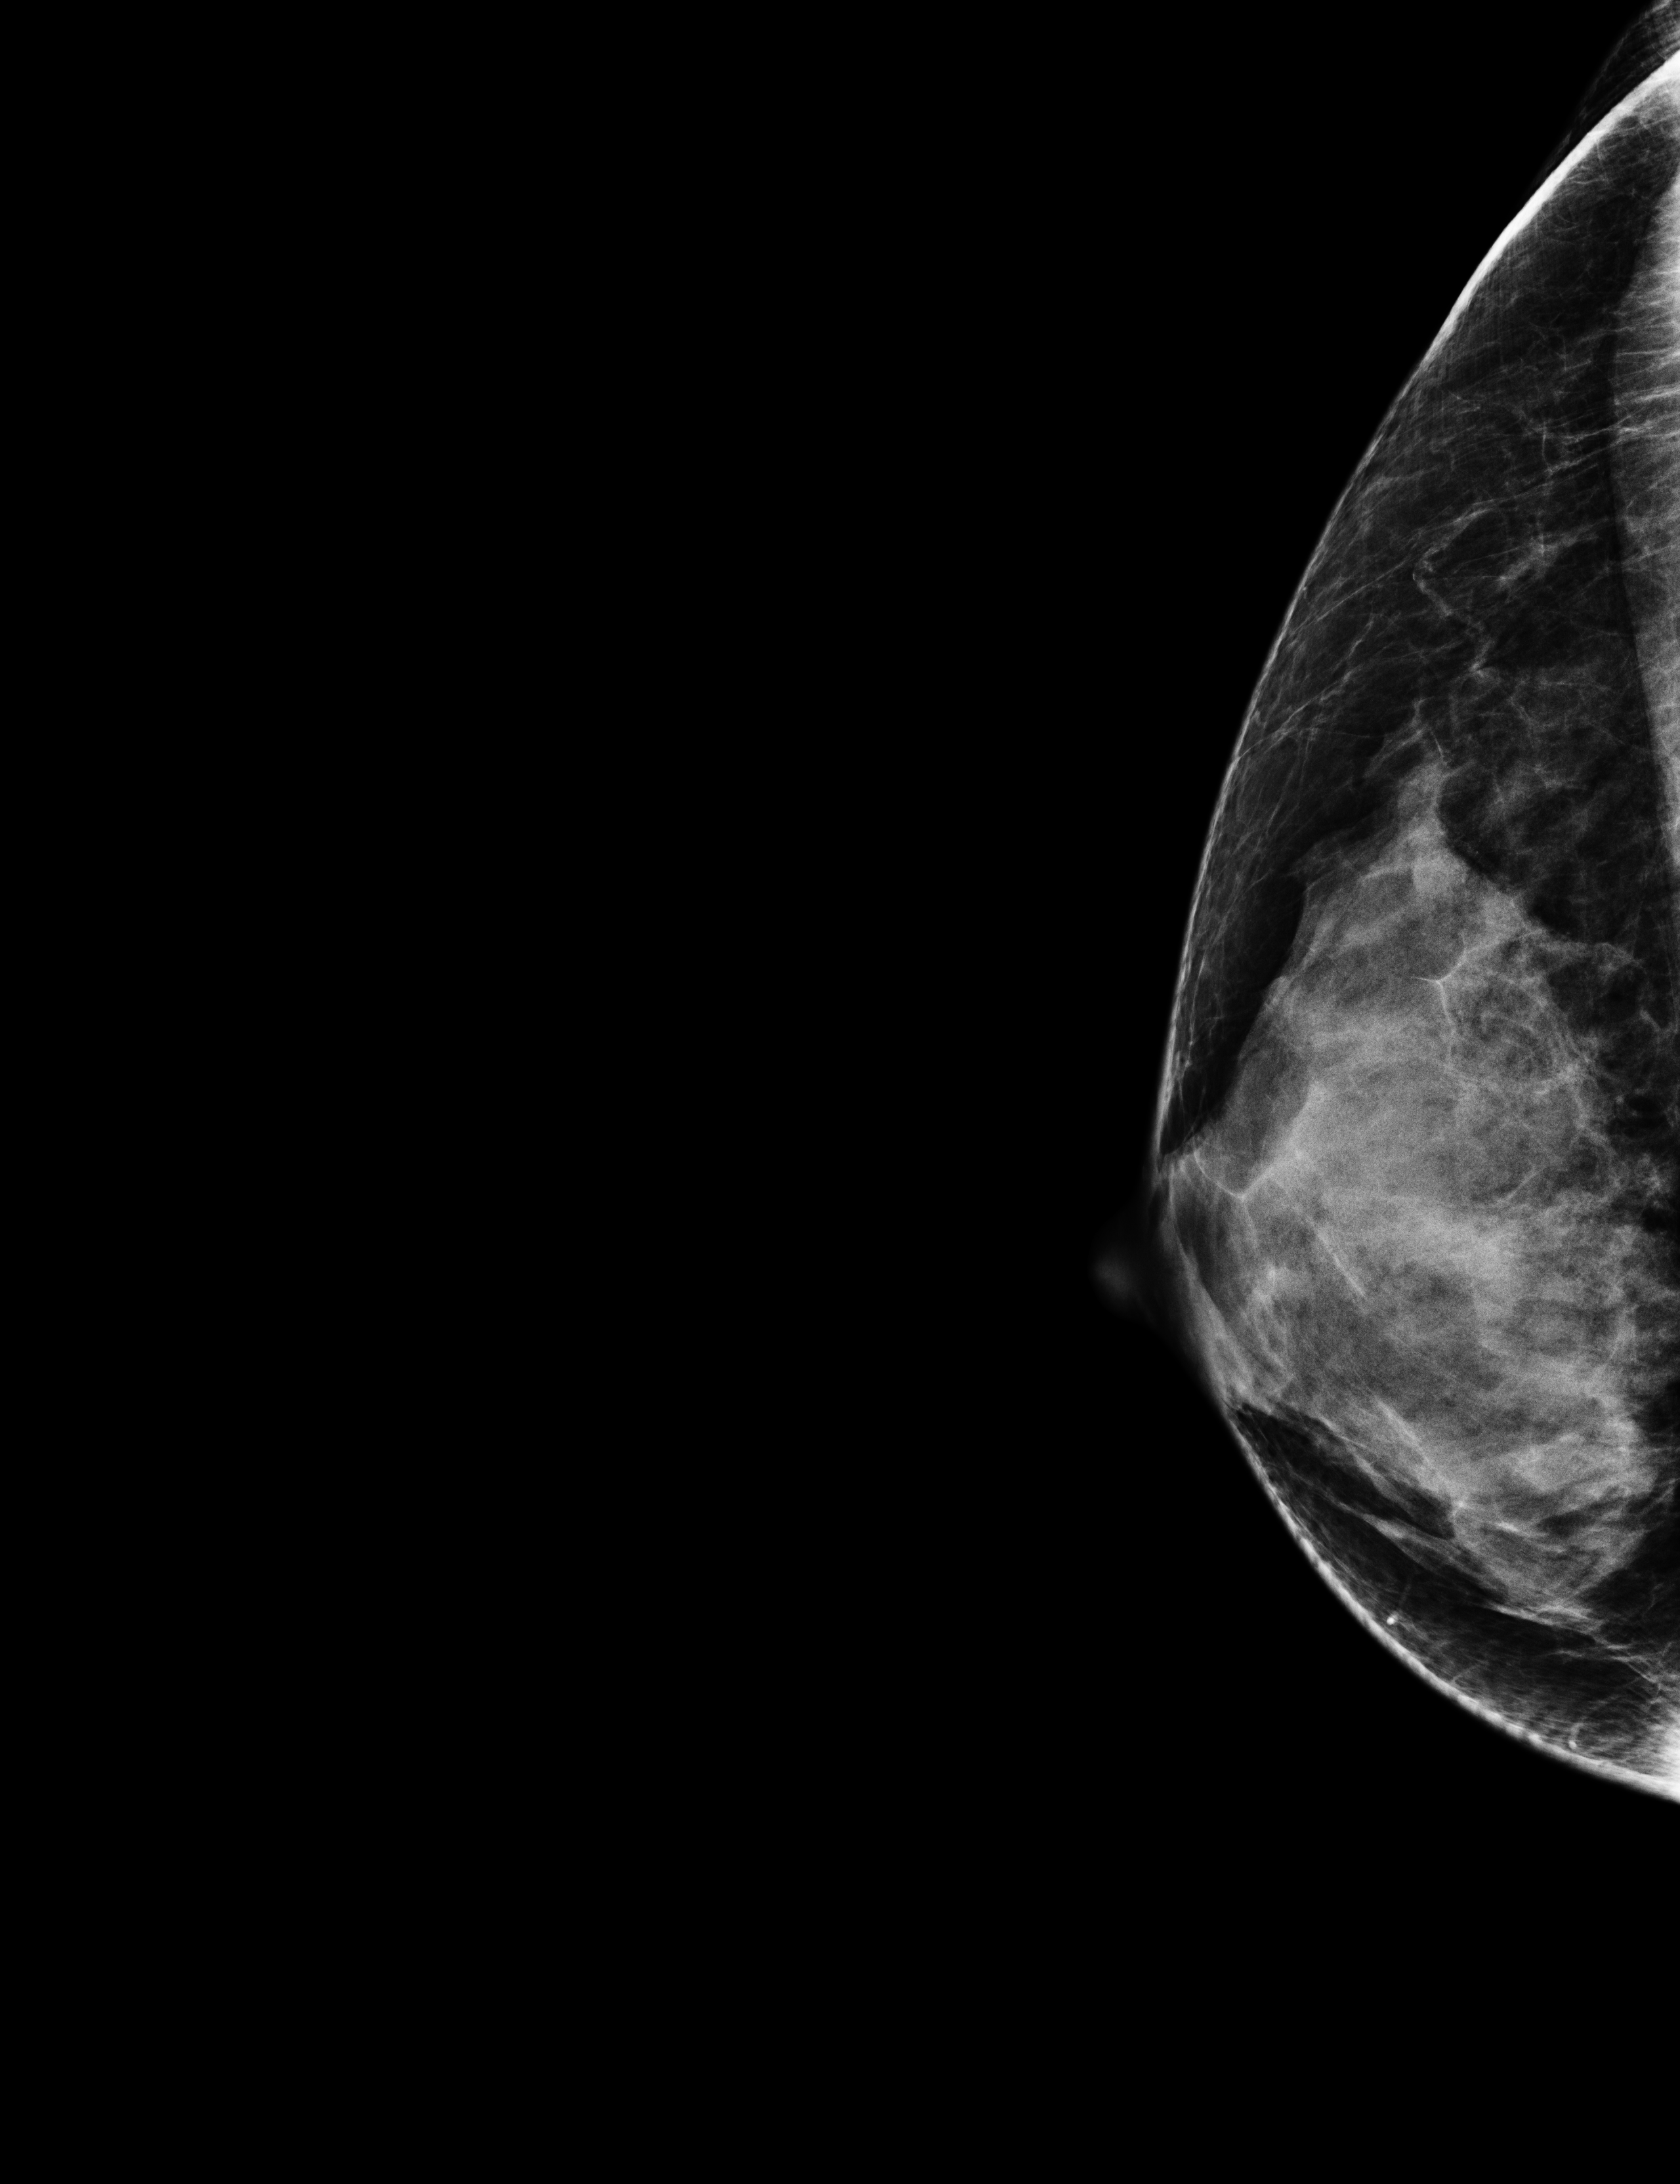
Screening examination; compressed breast thickness 44 mm; system: Selenia Dimensions. Patient: female, 66 years.
Image type: full-field digital mammogram. Breast: right. Projection: exaggerated CC view (lateral).